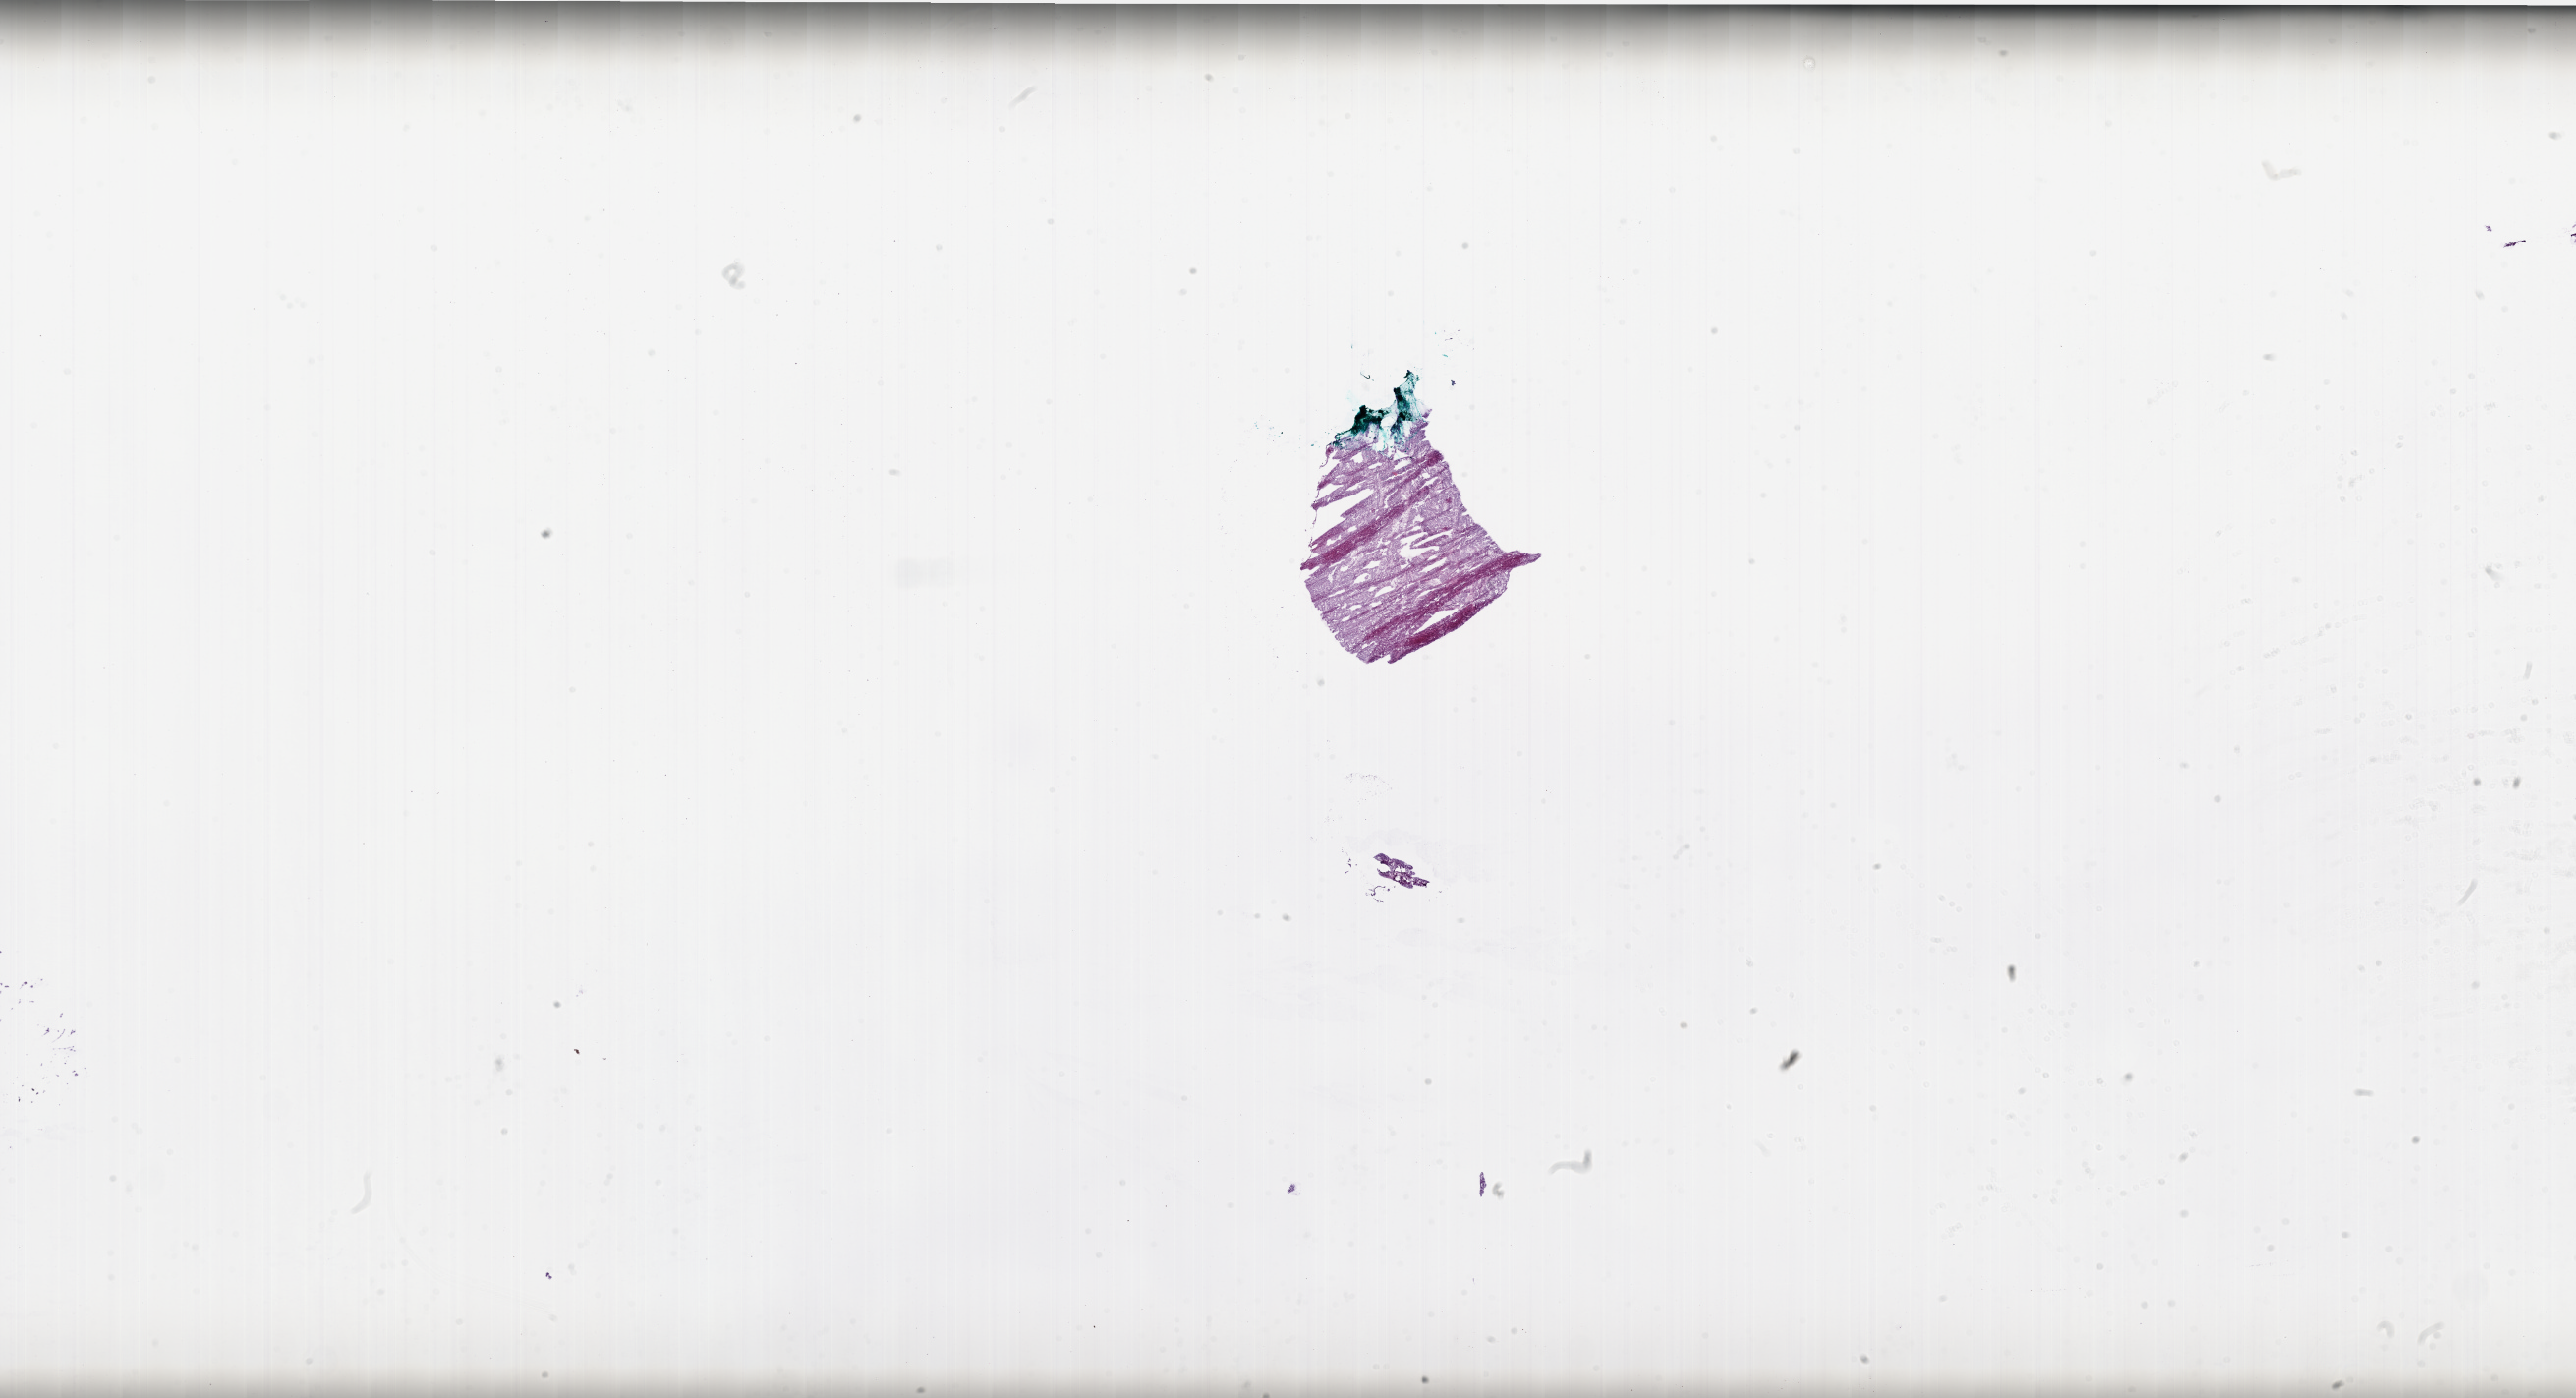
Digitized H&E-stained tissue section (whole slide) — low-resolution overview of the scanned area, about 42.0 x 22.8 mm (slide scanned at 20x); frozen section; primary tumour sample from the ovary. Patient: female, age at initial diagnosis 80 years. Histologic grade: G3 (poorly differentiated). Pathologist review of this section (percent, as recorded): tumour cells 90%, tumour nuclei 95%, normal cells 0%, stromal cells 10%, necrosis 0%.
- FIGO stage: IIC
- pathologic diagnosis: Serous cystadenocarcinoma, NOS